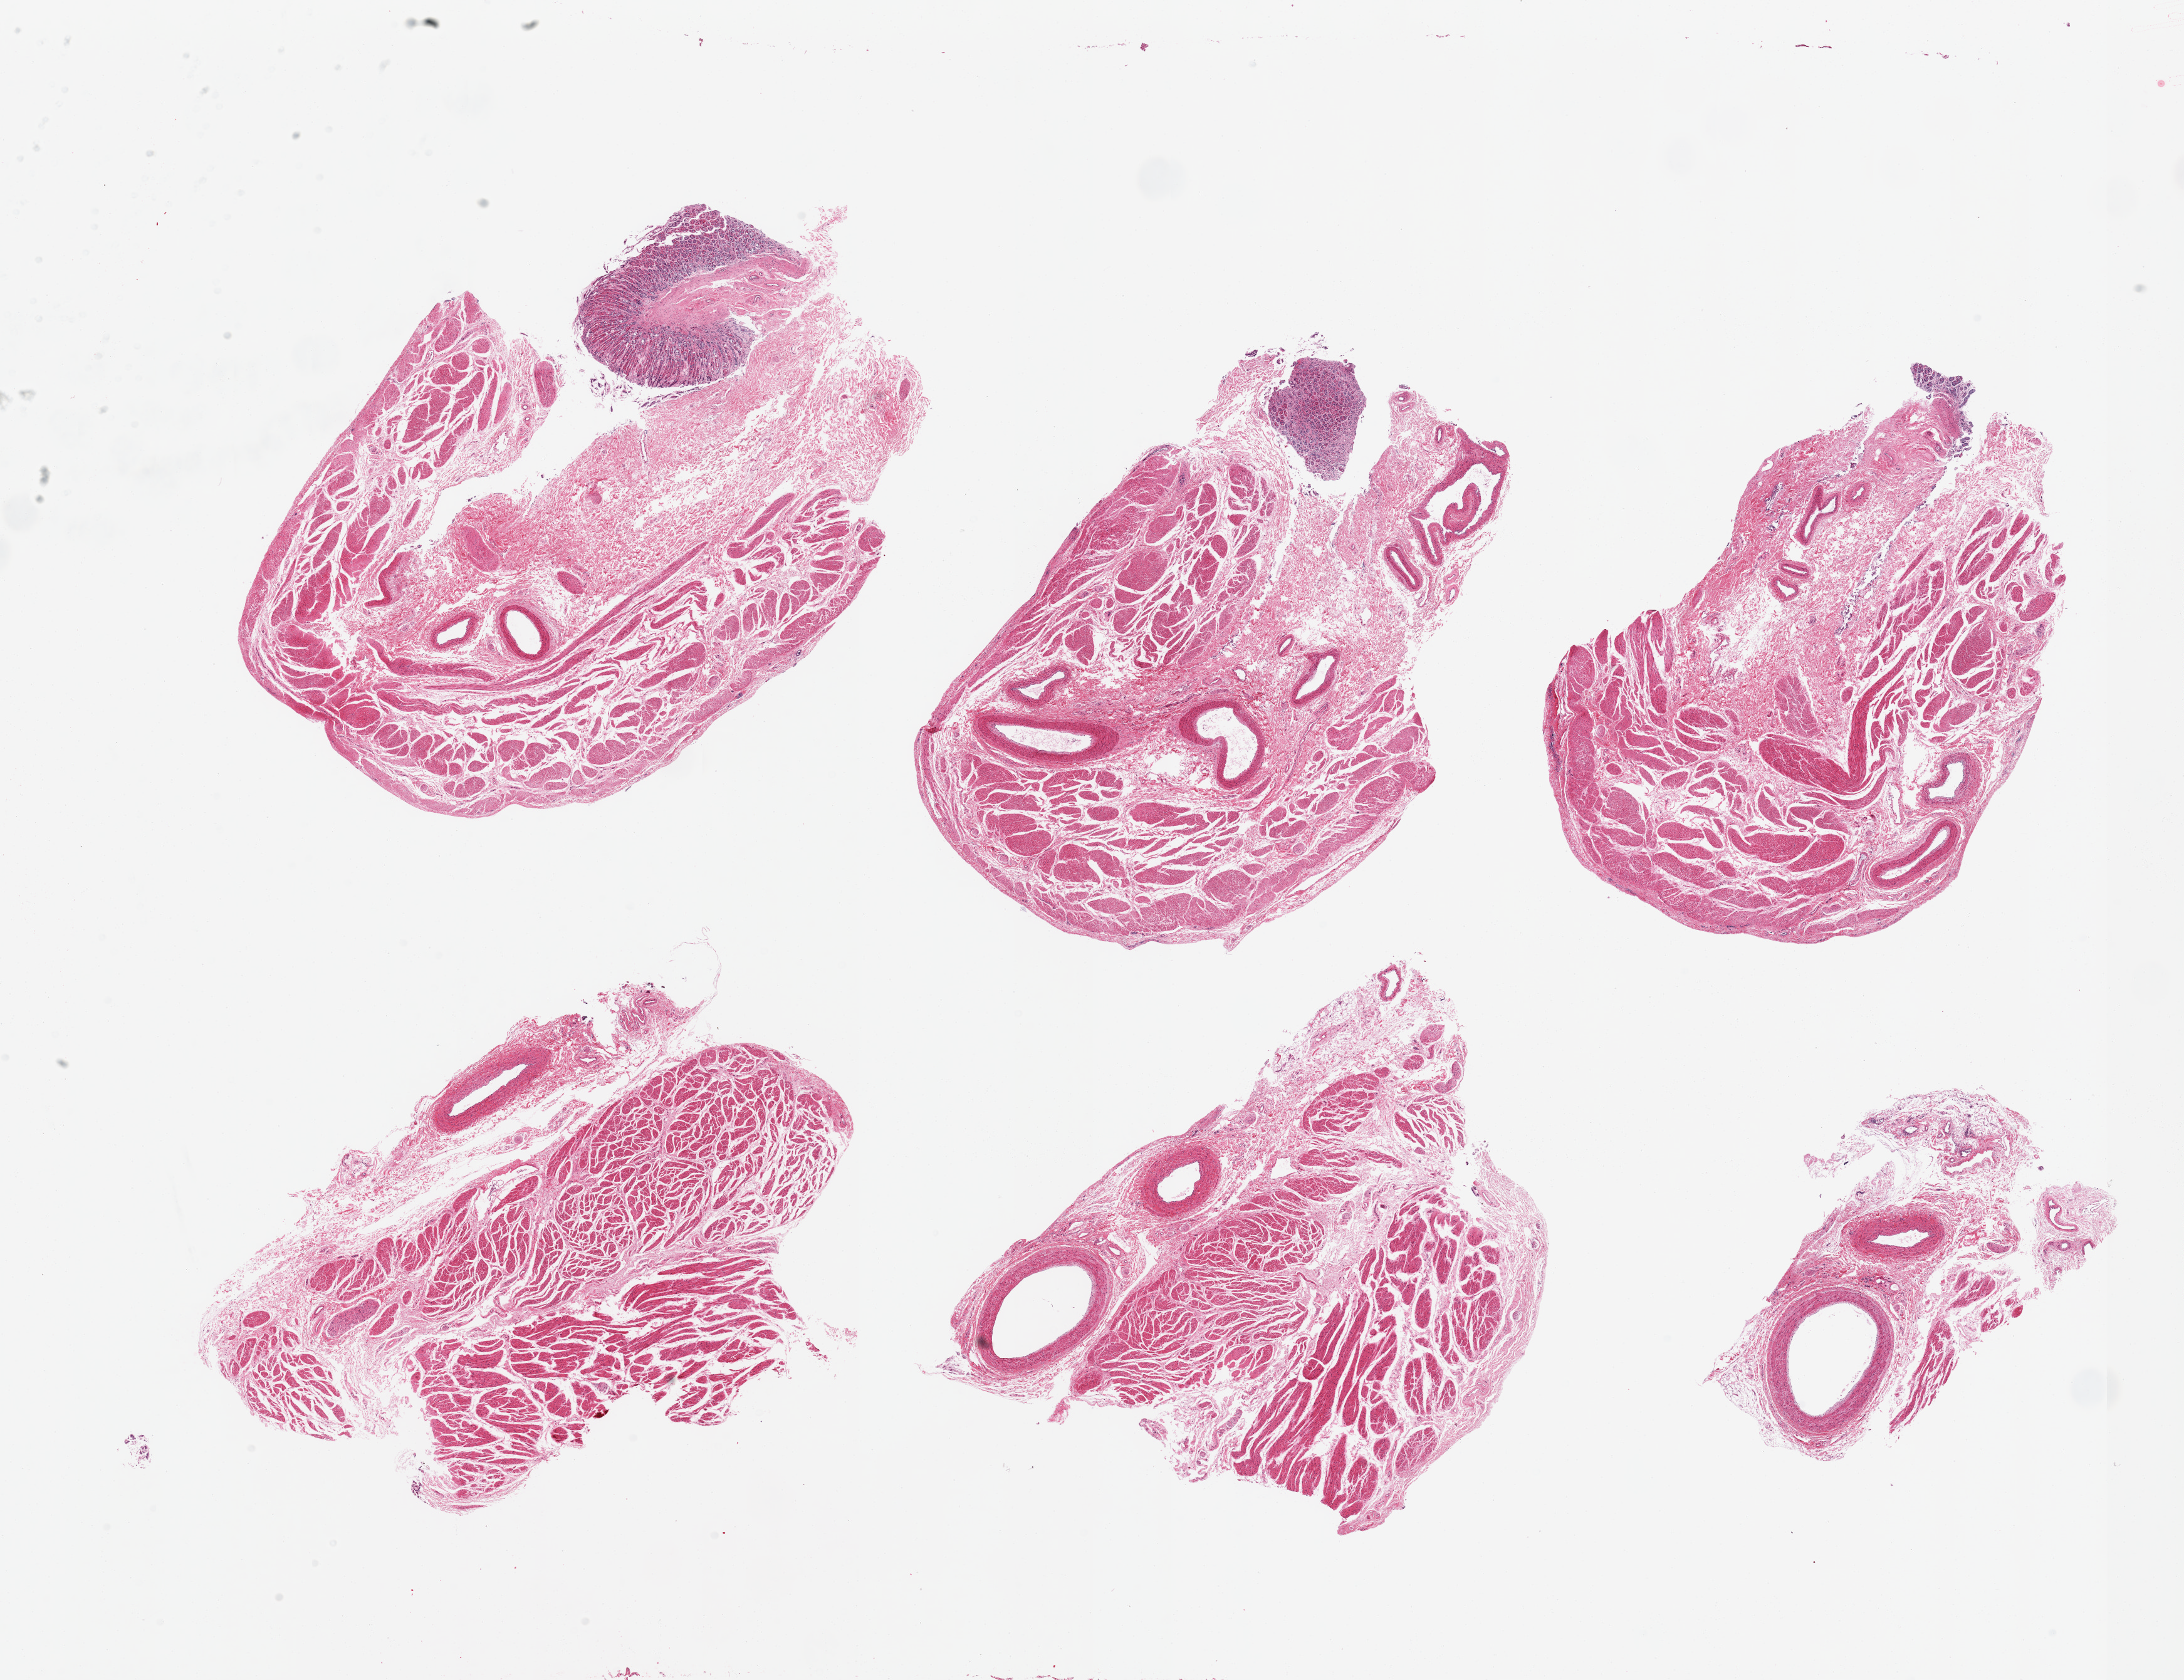
Digitized H&E-stained section — a low-resolution overview of the entire scanned area, about 27.6 x 21.2 mm. PAXgene-fixed paraffin-embedded (PFPE) section. Section of stomach (target tissue). Donor tissue sample.
• reviewer comment on this tissue sample: 6 pieces; mainly muscularis and tiny fragments of gastric mucosa